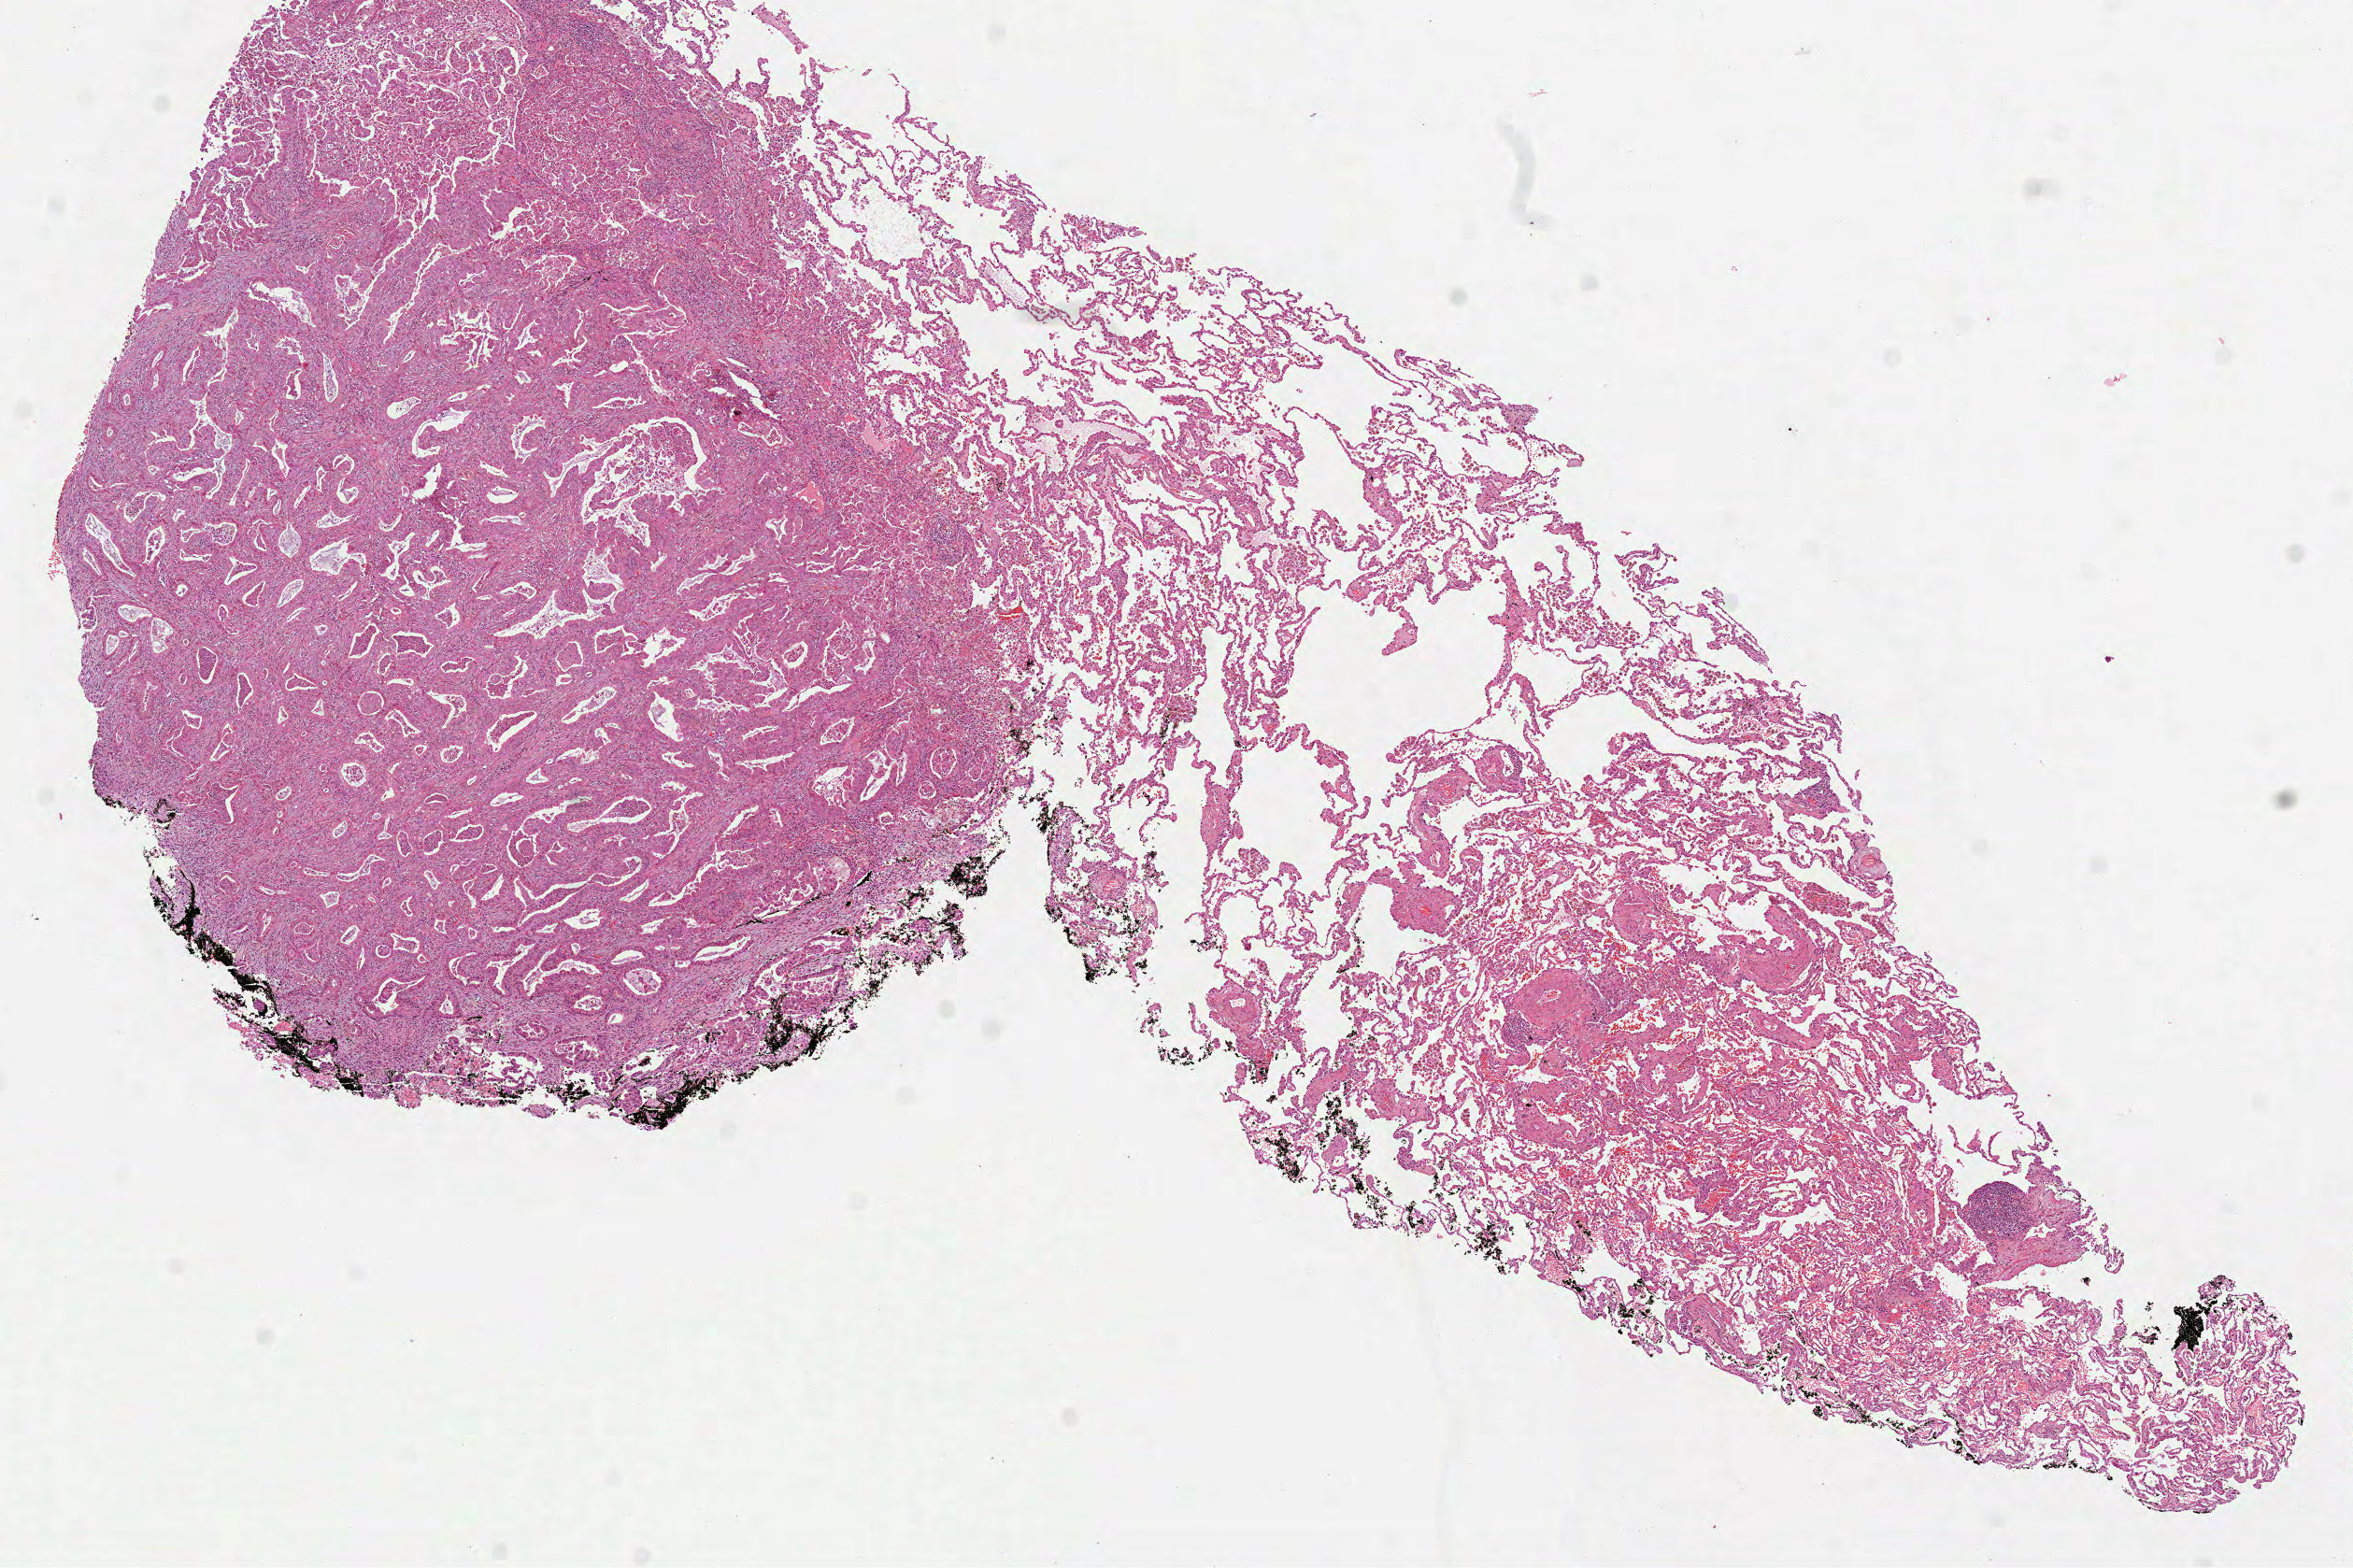
Digitized Hematoxylin and eosin (H&E) stained tissue section (whole slide), shown as a low-resolution overview of the whole scanned area (about 10.2 x 6.8 mm, from a 40x scan). FFPE section. Lung, primary tumour sample. Male patient; age at initial diagnosis 69 years.
TNM: T2b N0 M0. AJCC pathologic stage: IIA. Diagnosis: Adenocarcinoma, NOS.